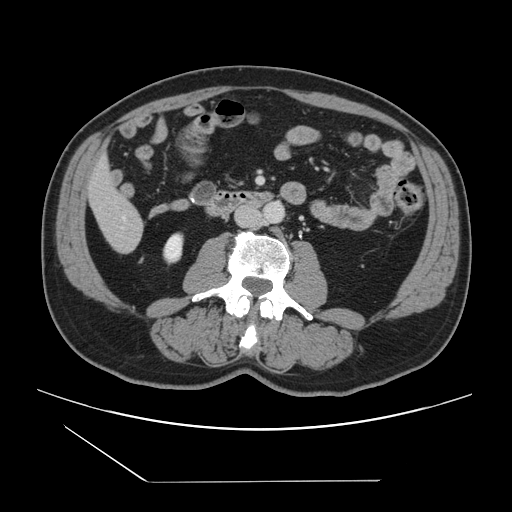
Contrast-enhanced abdominal CT, one axial slice; position 24 of 157 along the scan axis; 120 kVp; intravenous contrast given; soft-tissue window (W 400 / L 40 HU); 2.5 mm slice thickness; 512 × 512 image matrix. Male patient, age 61 years. Case-level facts recorded for this patient, not image findings: diagnosis: colorectal cancer liver metastases, imaged before liver resection; multiple liver metastases: yes; largest metastasis: 5.5 cm.
Structures marked on this image (expert manual segmentation):
- liver: bounding box [x1, y1, x2, y2] px = [90, 160, 143, 252]
- planned liver remnant (the part of the liver to remain after resection): [90, 160, 134, 218]